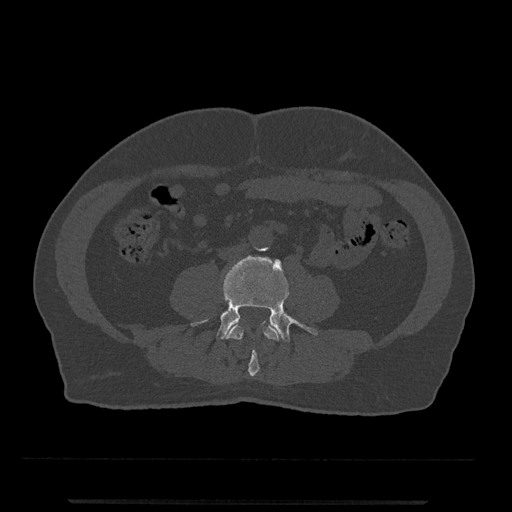
CT including the spine, one axial slice. Position 159 of 797 along the scan axis. 120 kVp. Bone window (W 1800 / L 400 HU). 0.5 mm slice thickness. 512 × 512 image matrix. Patient: male, 63 years. Case-level facts recorded for this patient, not image findings: primary cancer: prostate.
Structures marked on this image (semi-automatically segmented with operator editing):
- L3 vertebra: bounding box (x1, y1, x2, y2) in pixels: (226, 321, 281, 377)
- L4 vertebra: (191, 256, 318, 342)